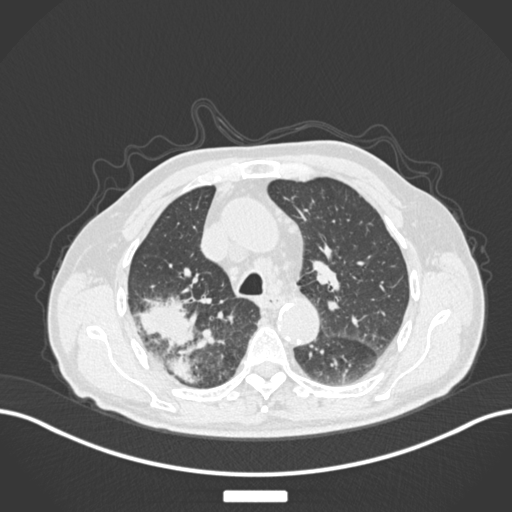
Chest CT, one axial slice; slice 129 of 201 in the series (ordered by position); reconstruction kernel B30f; lung window (W 1500 / L -600 HU); 1 mm slice thickness; 512 × 512 image matrix. Male patient, age 72 years. Case-level facts recorded for this patient, not image findings: clinical TNM (as recorded): T3 N2 M0.
Annotated regions visible in this slice (bounding box drawn by a radiologist):
- lung tumour (recorded histology: adenocarcinoma): bounding box <133,291,205,386> (left, top, right, bottom; pixels)